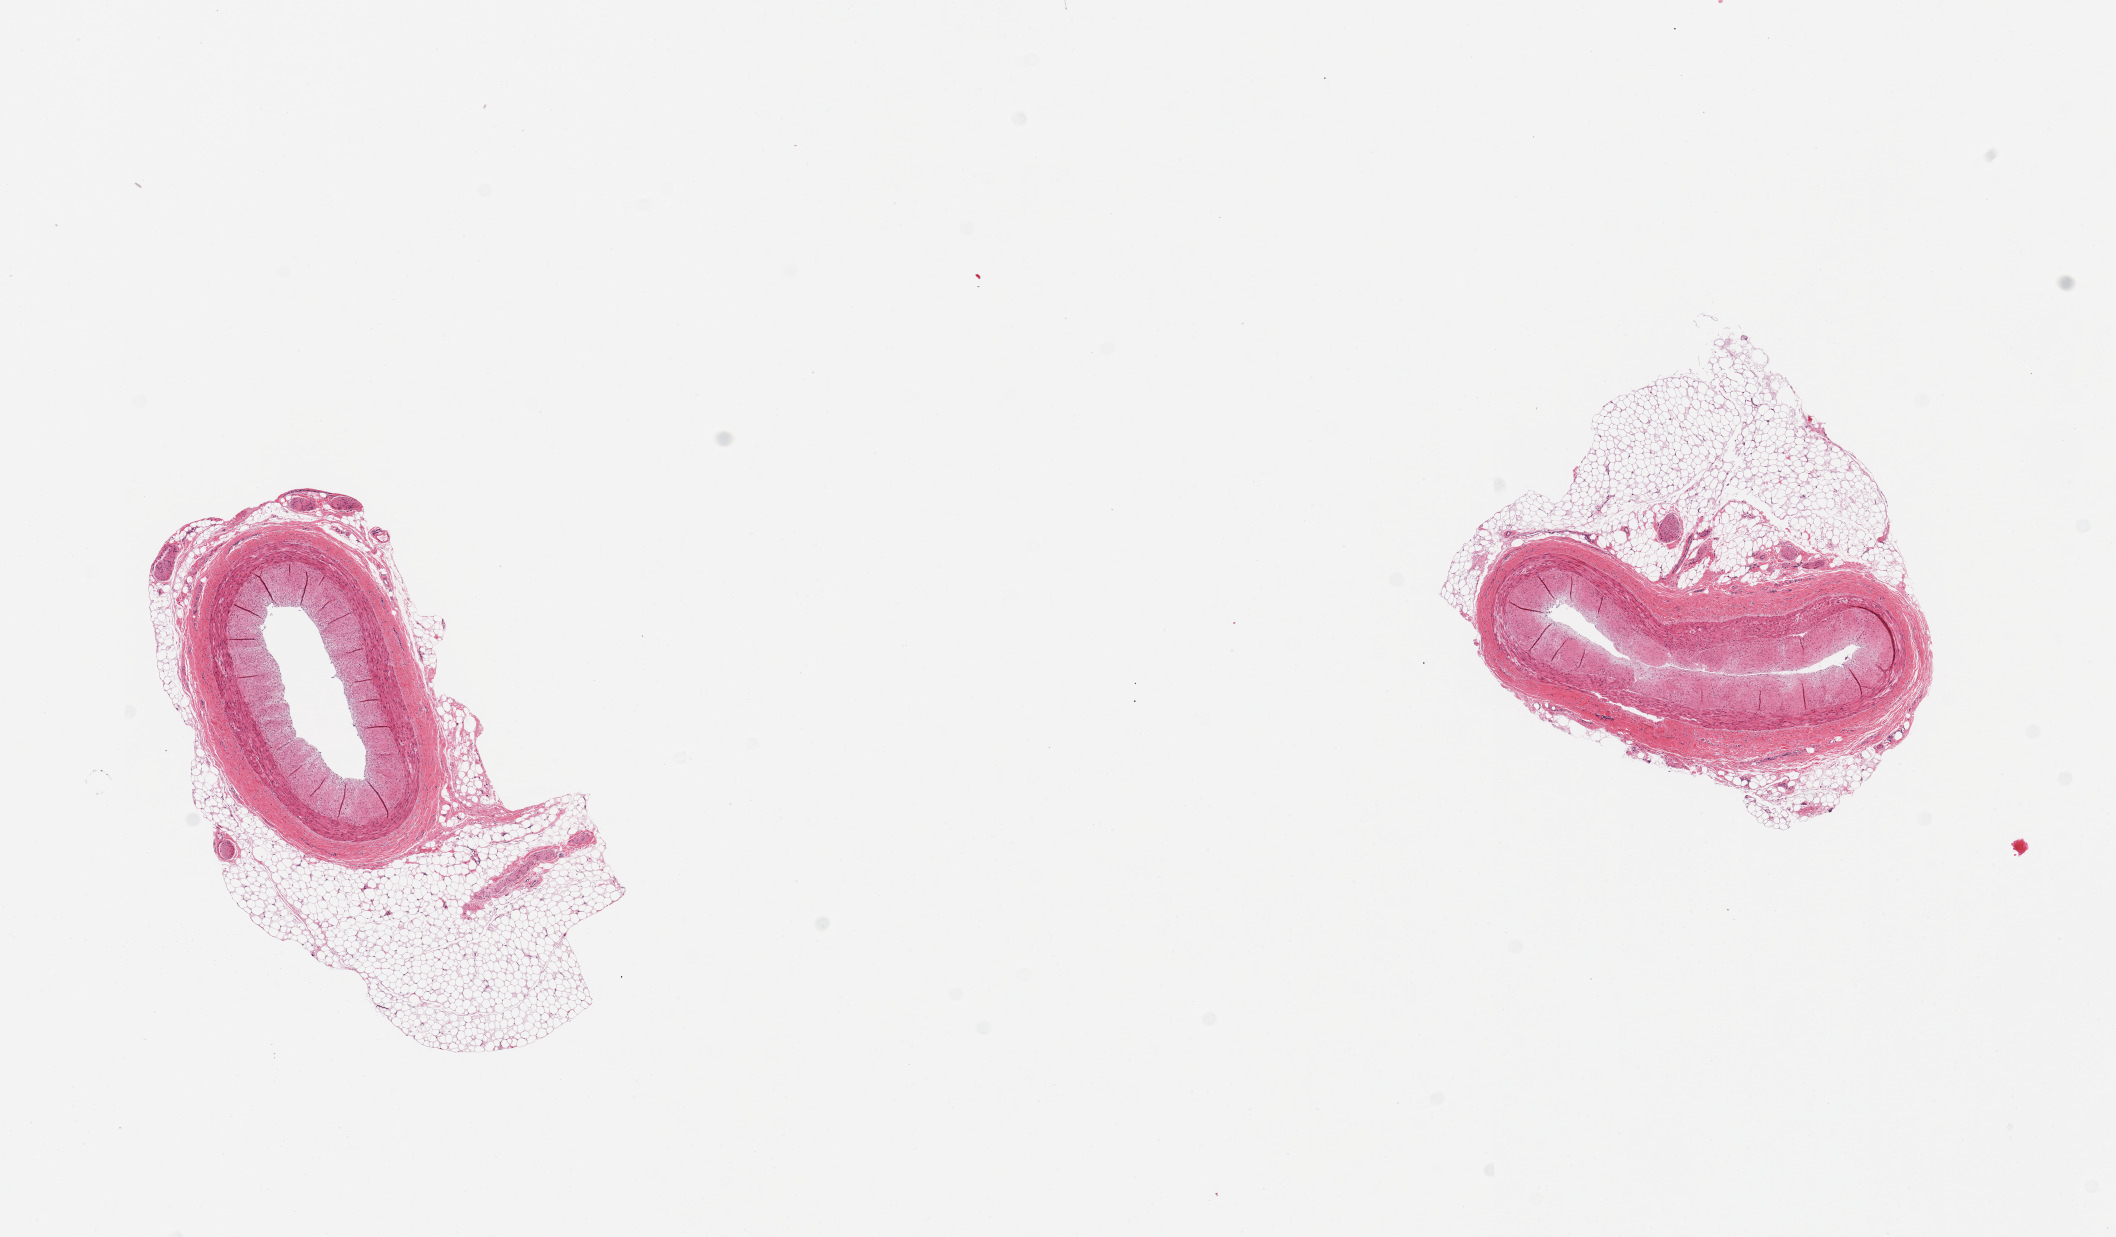
Haematoxylin and eosin whole-slide image — shown as a low-resolution overview of the whole scanned area (about 16.7 x 9.8 mm), PAXgene-fixed paraffin-embedded (PFPE) section, section of coronary artery (target tissue), tissue donor sample. Donor: female.
* review note (as recorded): 2 pieces, no atherosis, adherent fat up to ~2mm